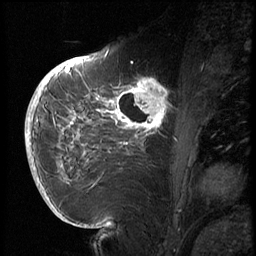
Breast MRI (dynamic contrast-enhanced), one sagittal slice; slice 27 of 72 in the series (ordered by position); 3 images stored at this slice position (order not interpretable as contrast timing); 1.5 T; TE 4.2 ms, TR 8.9 ms; 2.5 mm slice thickness; 256 × 256 image matrix, field of view 200 × 200 mm. Female patient, age 56 years. Case-level facts recorded for this patient, not image findings: setting: breast cancer imaged before/during neoadjuvant chemotherapy.
Outlined on this slice (semi-automatically segmented with operator editing):
- analysis volume of interest (the breast-tissue region the enhancement analysis was run in; not a lesion): bounding box <114,76,177,138> (left, top, right, bottom; pixels)
- tumour enhancement mask (voxels above the 140 % enhancement threshold inside the analysis volume of interest): <114,78,171,130>